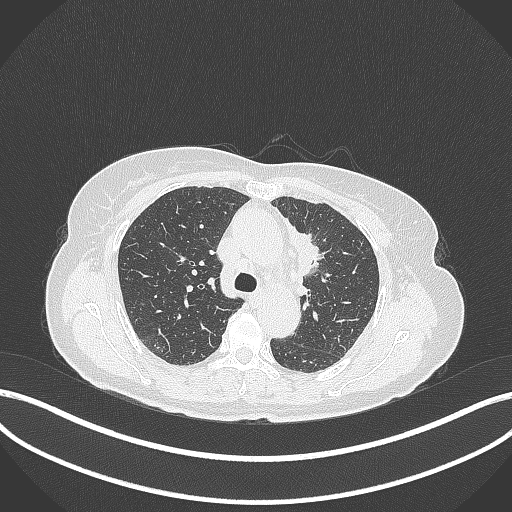
Chest CT, one axial slice; slice 231 of 369 in the series (ordered by position); lung window (W 1500 / L -600 HU); 1 mm slice thickness; 512 × 512 image matrix, field of view 400 × 400 mm. Female patient, age 65 years. Case-level facts recorded for this patient, not image findings: clinical TNM (as recorded): T2a N0 M0; histopathological grade: G2-3.
Outlined on this slice (bounding box drawn by a radiologist):
- lung tumour (recorded histology: adenocarcinoma): bounding box (x1, y1, x2, y2) in pixels: (282, 222, 325, 279)